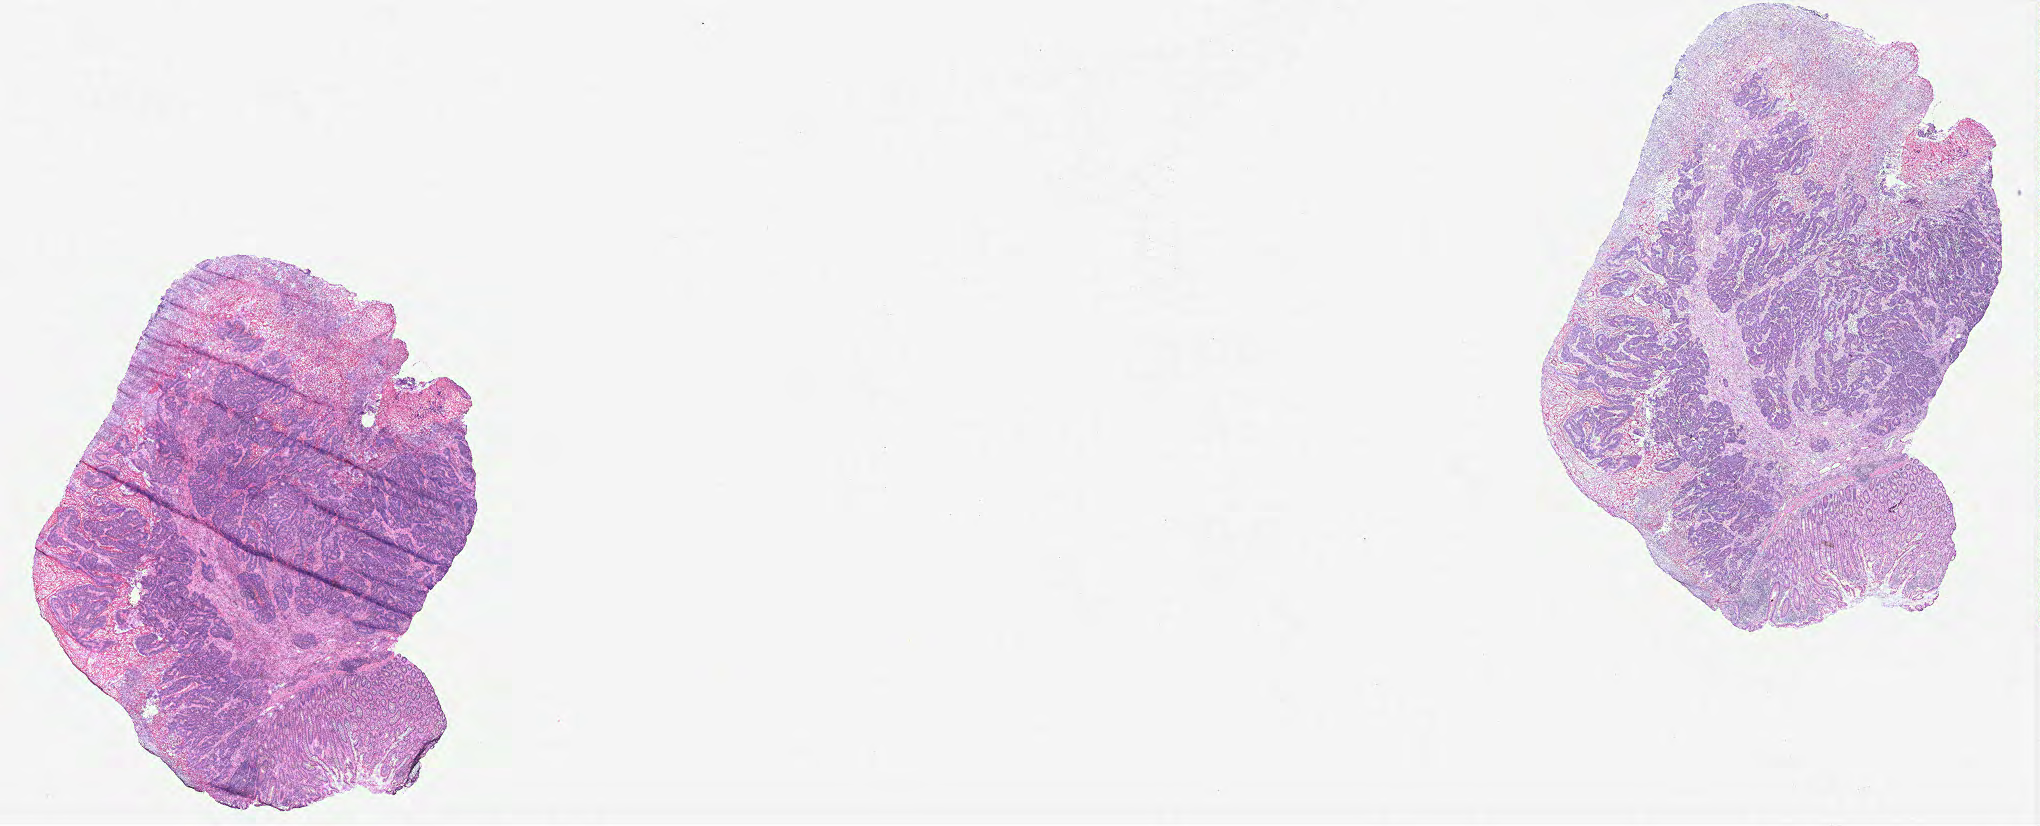
Whole-slide histology image, H&E-stained — a low-resolution overview of the entire scanned area, about 32.7 x 13.2 mm (acquisition: 40x scan). Normal (non-tumour) tissue sample, colon. 66-year-old female patient.
This section: normal (non-tumour) tissue from the same patient. Patient diagnosis: Adenocarcinoma, NOS.